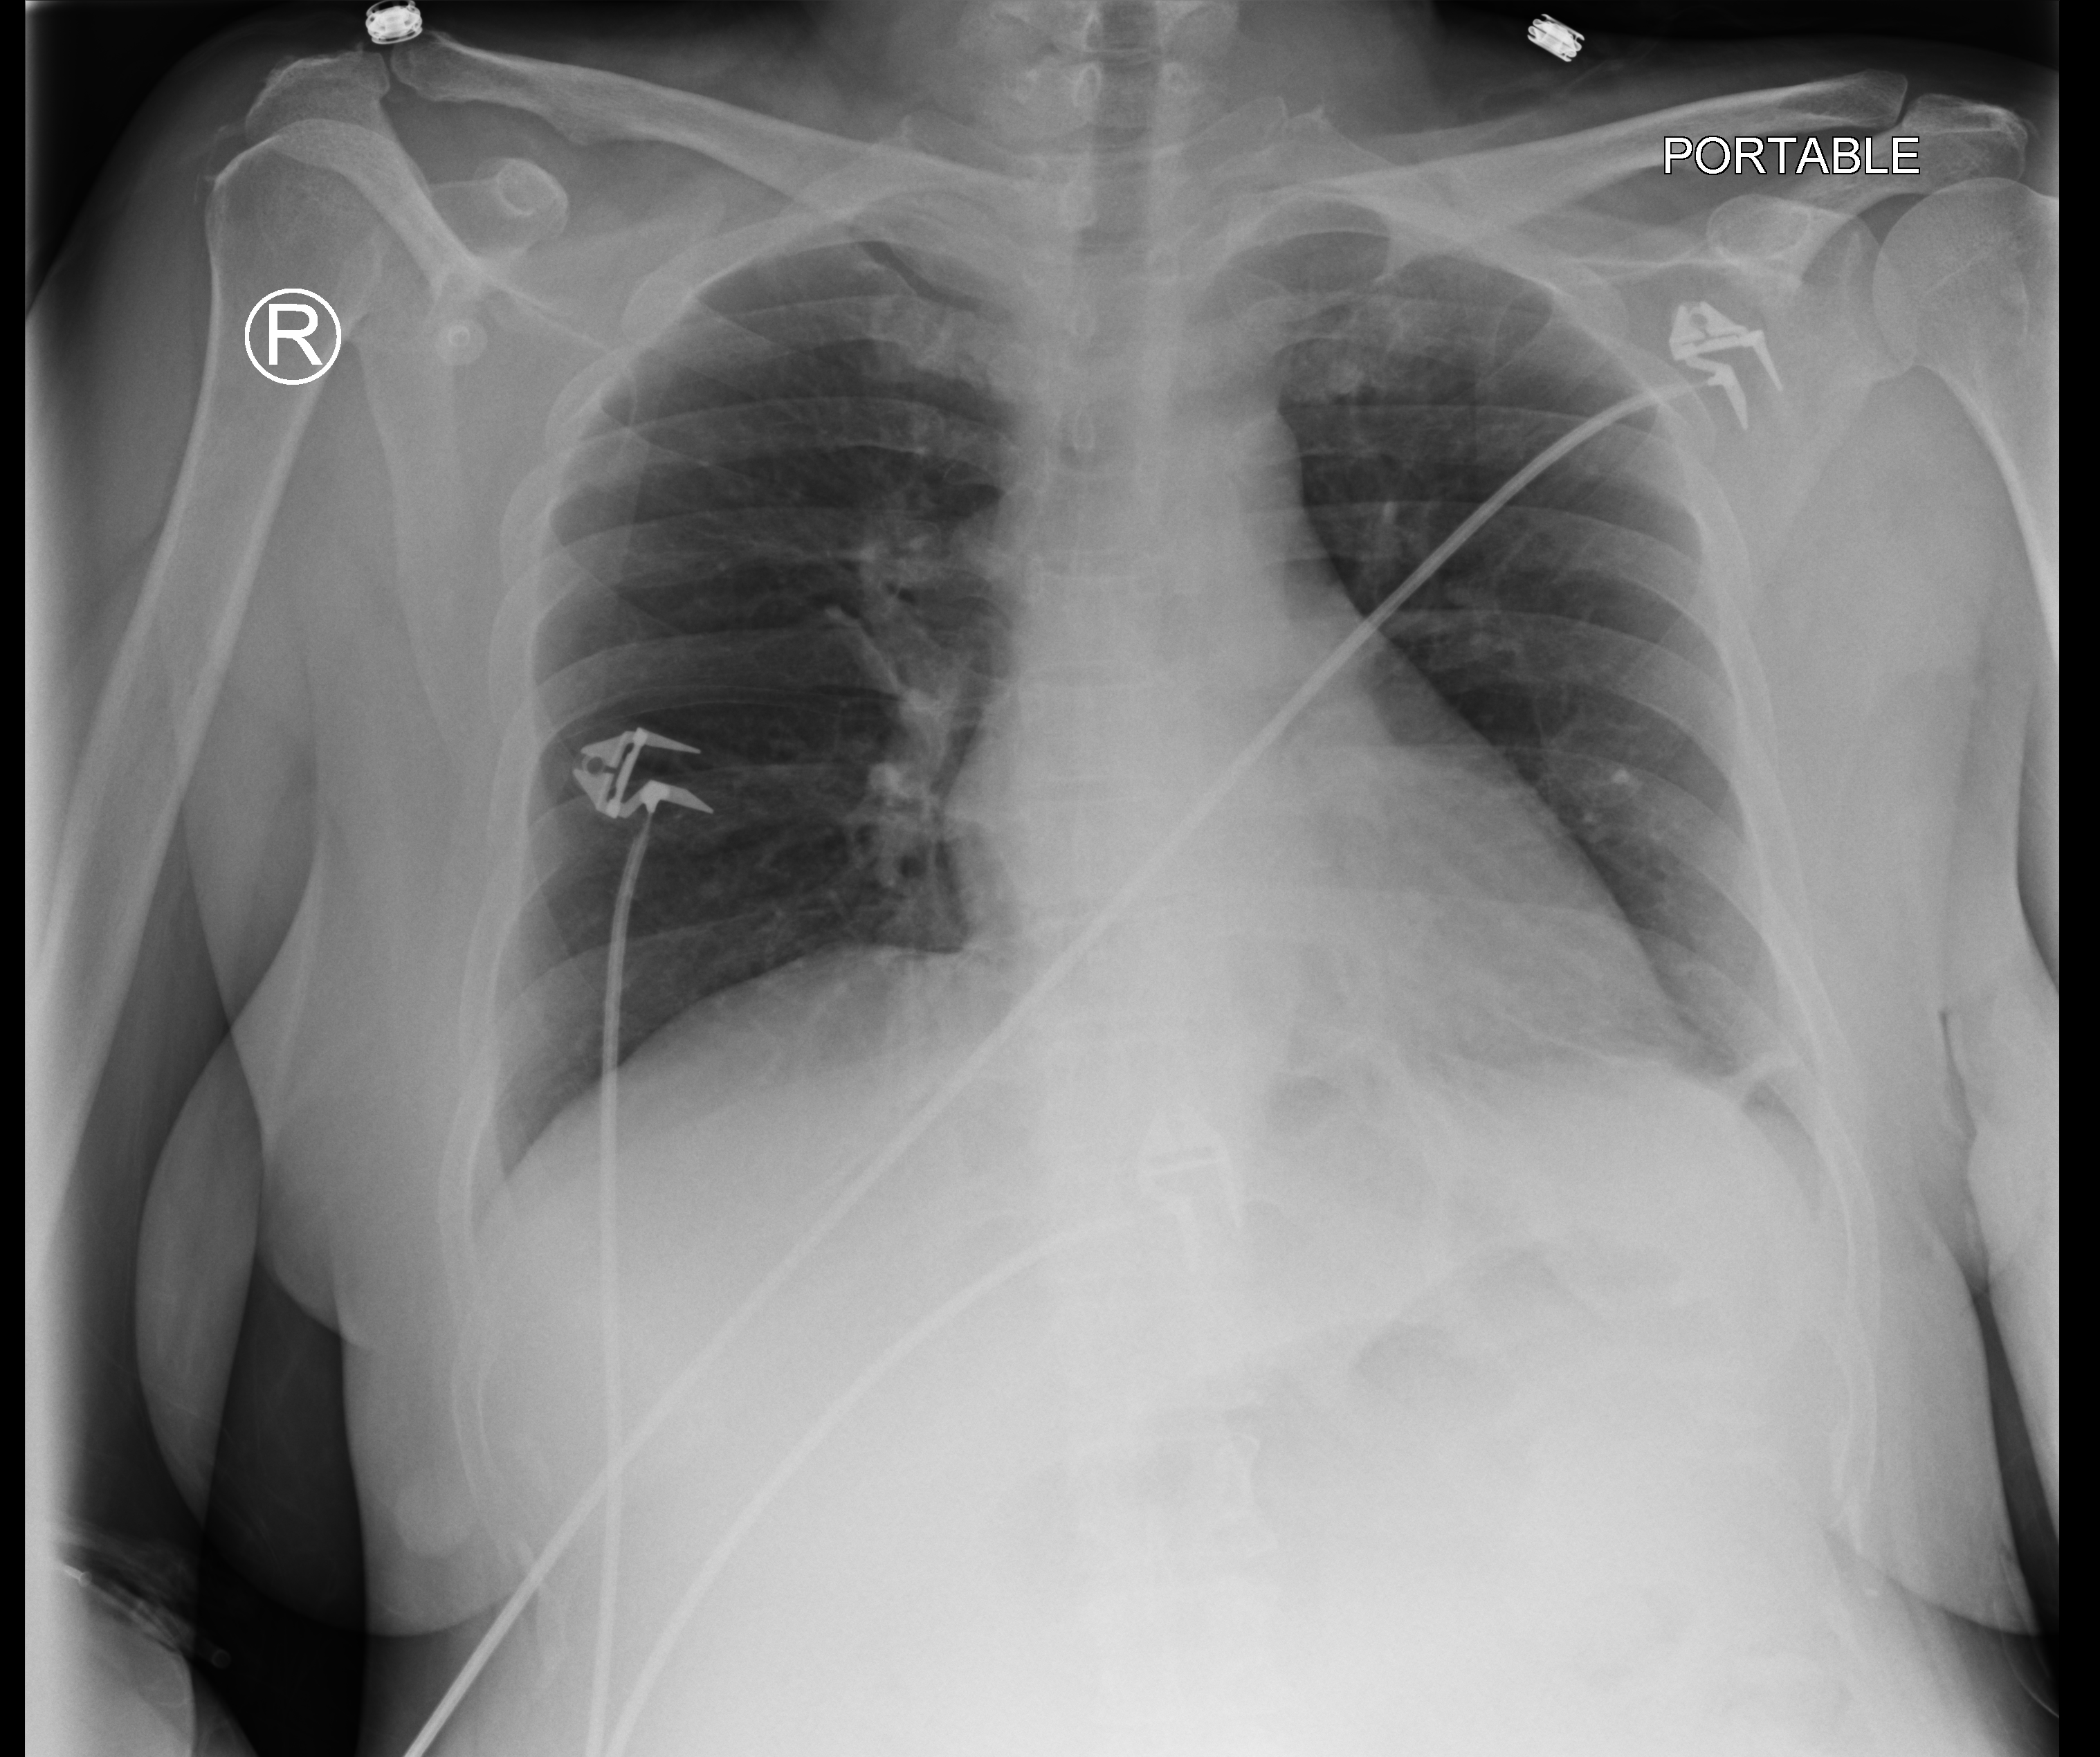
Chest X-ray (portable); anteroposterior (AP) projection. Female patient hospitalised with COVID-19, age 18–59 years.
From the hospital-stay record, not from the radiograph (when in the stay this image was taken is not recorded):
- mechanically ventilated during this hospital stay: no
- admitted to intensive care during this hospital stay: no
- diabetes (admission record): yes